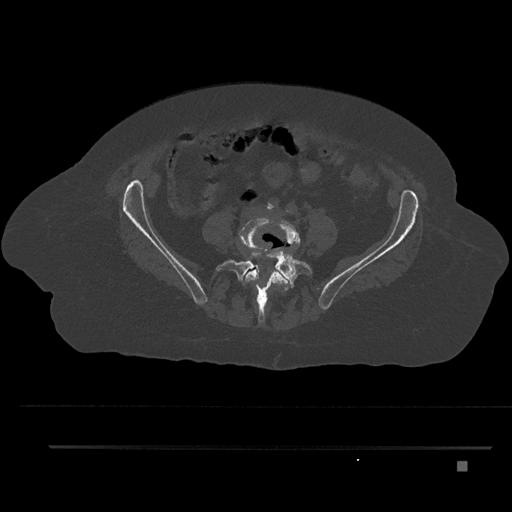
CT including the spine, one axial slice; position 54 of 797 along the scan axis; reconstruction kernel Br40s/3; bone window (W 1800 / L 400 HU); 512 × 512 image matrix, field of view 437 × 437 mm. Patient: female, 76 years. Case-level facts recorded for this patient, not image findings: primary cancer: lung.
Annotated regions visible in this slice (semi-automatically segmented with operator editing):
- L4 vertebra: box from (x=239, y=215) to (x=300, y=310) px
- L5 vertebra: (x=216, y=235)–(x=312, y=323)